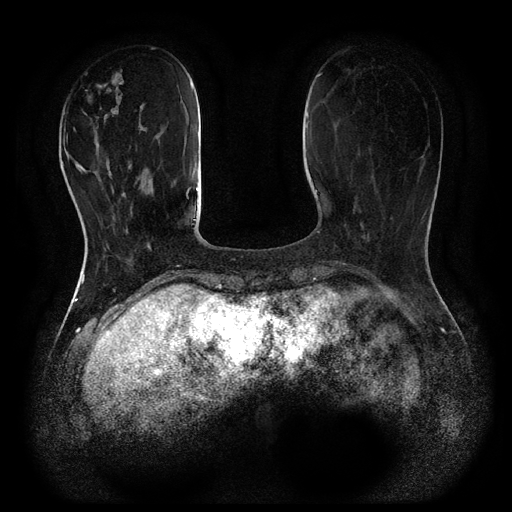
Breast MRI (dynamic contrast-enhanced, multi-phase), one axial slice; slice 27 of 116 in the series (ordered by position); dynamic contrast-enhanced series, time point 2 of 5 at this slice position (early post-contrast); 1.5 T; TE 2.6 ms, TR 5.4 ms; 2 mm slice thickness; 512 × 512 image matrix, field of view 340 × 340 mm. Female patient, age 48 years.
Annotated regions visible in this slice (semi-automatic segmentation, software-assisted and operator-edited):
- breast lesion (labelled benign in the annotation): bounding box [x1, y1, x2, y2] px = [80, 68, 124, 134]